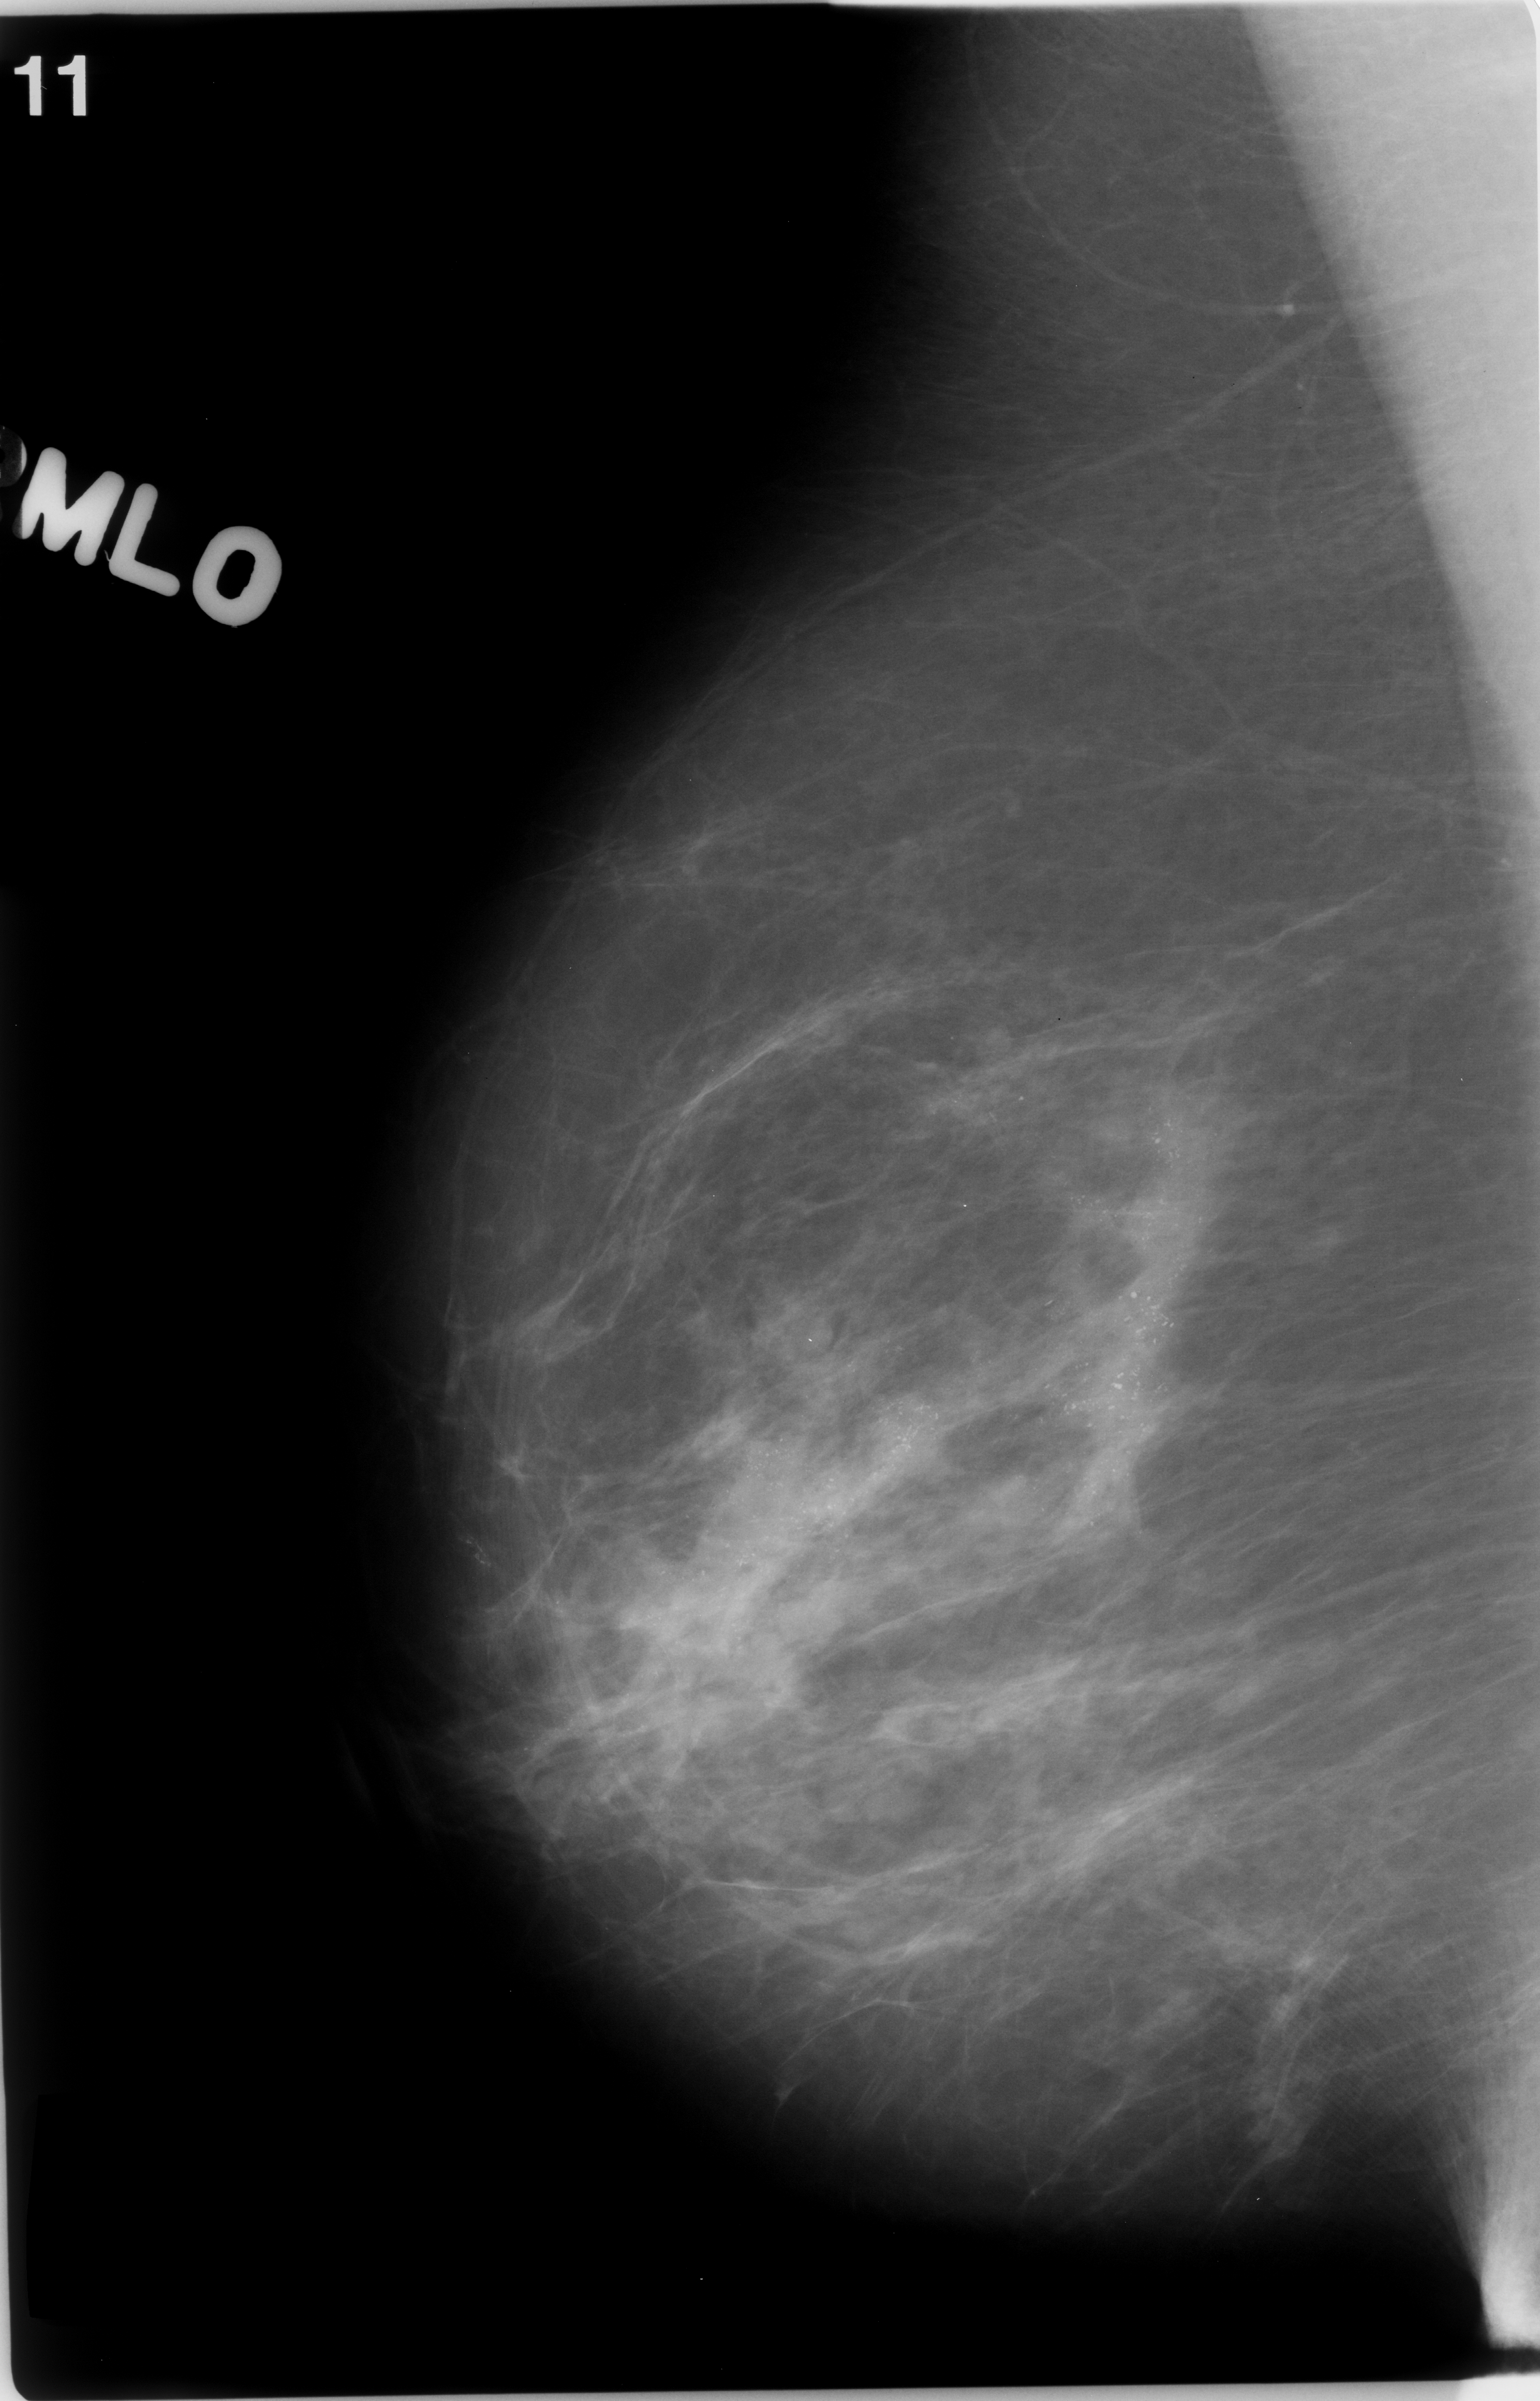
Mammogram (digitized film); right breast; MLO view; BI-RADS breast density category 2 (scale 1–4); 1540 × 2401 image matrix.
Expert-marked regions of interest on this film, with their recorded descriptors:
- calcifications, morphology pleomorphic, distribution regional; BI-RADS assessment category 5; subtlety rating 5 on a 1 (subtle) to 5 (obvious) scale; pathology (as recorded): malignant: bounding box [x1, y1, x2, y2] px = [521, 989, 1231, 1839]